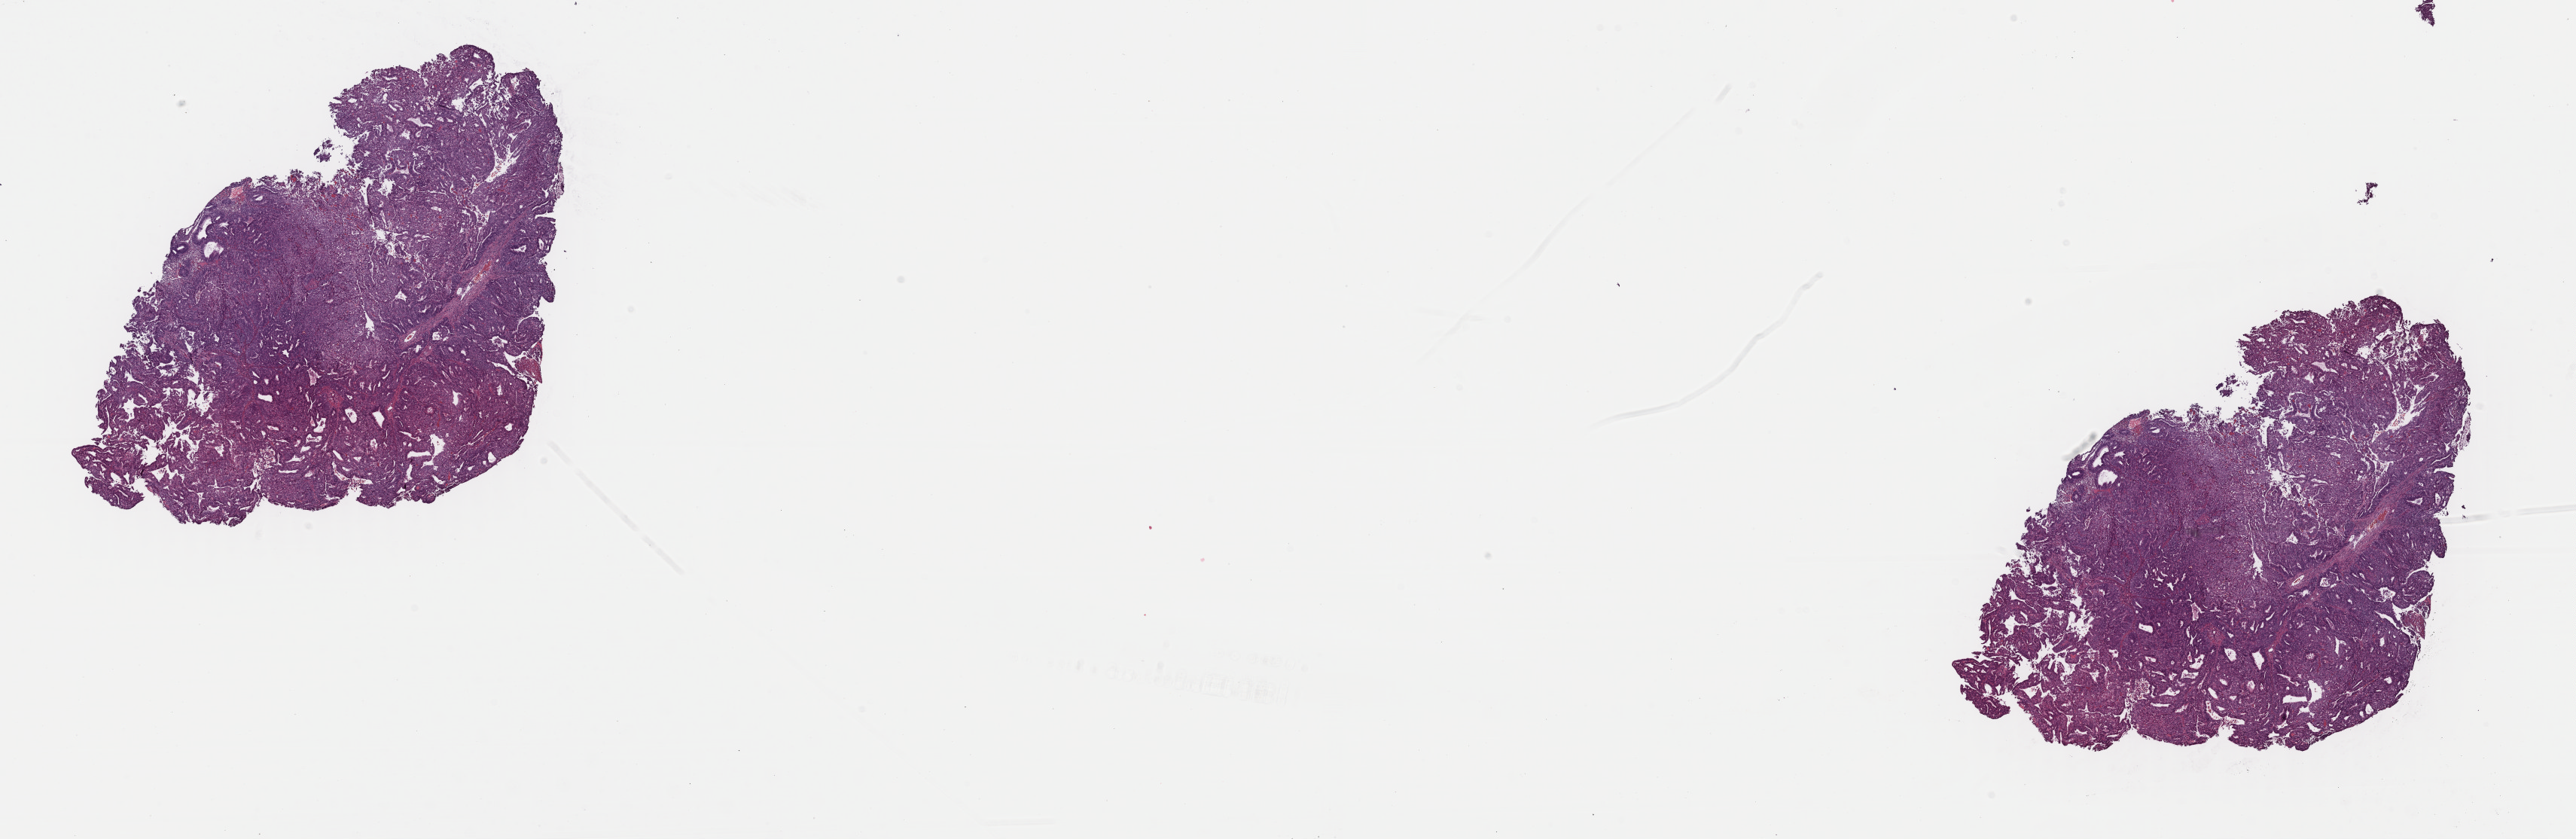
H&E whole-slide image, a low-resolution overview of the entire scanned area, about 27.0 x 8.8 mm (from a 40x scan); formalin-fixed paraffin-embedded (FFPE) diagnostic section; uterus, primary tumour sample. Patient: female, age at initial diagnosis 47 years. Histologic grade: G2 (moderately differentiated).
• diagnosis: Endometrioid adenocarcinoma, NOS (endometrium)
• FIGO stage: IB